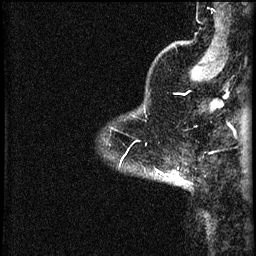
Breast MRI (dynamic contrast-enhanced), one sagittal slice; slice 7 of 60 in the series (ordered by position); 3 images stored at this slice position (order not interpretable as contrast timing); 1.5 T; TE 4.2 ms, TR 8.2 ms; 256 × 256 image matrix, field of view 200 × 200 mm. Patient: female, 37 years.
Outlined on this slice (semi-automatic segmentation, software-assisted and operator-edited):
- analysis volume of interest (the breast-tissue region the enhancement analysis was run in; not a lesion): box from (x=150, y=168) to (x=189, y=189) px
- tumour enhancement mask (voxels above the 70 % enhancement threshold inside the analysis volume of interest): (x=162, y=174)–(x=177, y=179)